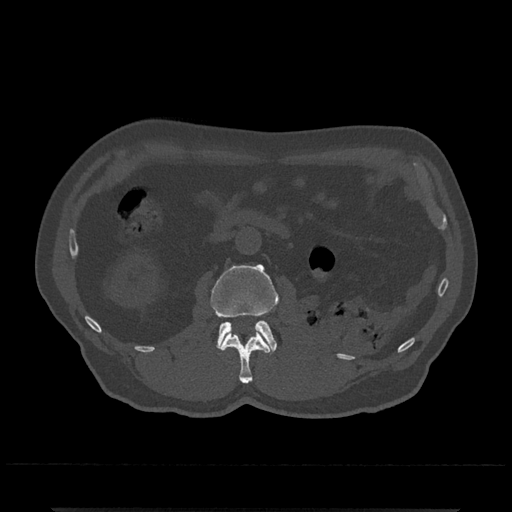
CT including the spine, one axial slice; slice 320 of 797 in the series (ordered by position); reconstruction kernel Br40s/3; bone window (W 1800 / L 400 HU); 0.5 mm slice thickness; 512 × 512 image matrix, field of view 393 × 393 mm. Patient: male, 67 years. From the clinical record (not read from this slice): primary cancer: prostate.
Outlined on this slice (semi-automatically segmented with operator editing):
- L1 vertebra: box from (x=220, y=331) to (x=270, y=384) px
- L2 vertebra: (x=210, y=264)–(x=278, y=353)